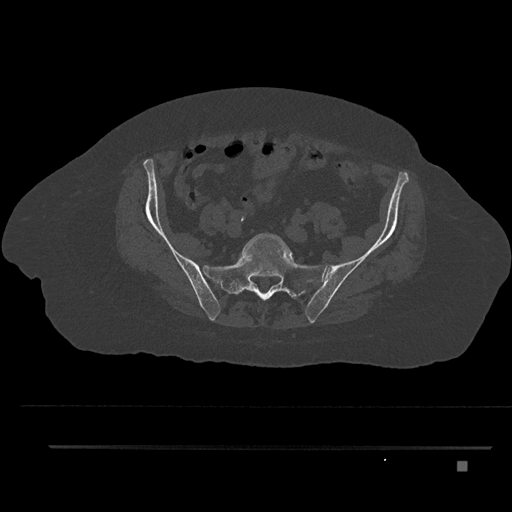
CT including the spine, one axial slice. Slice 8 of 797 in the series (ordered by position). Reconstruction kernel Br40s/3. Bone window (W 1800 / L 400 HU). 512 × 512 image matrix. Female patient, age 76 years. Case-level facts recorded for this patient, not image findings: primary cancer: lung; vertebrae with lytic lesions (as recorded): T11, L3.
Annotated regions visible in this slice (semi-automatically segmented with operator editing):
- L5 vertebra: bounding box [x1, y1, x2, y2] px = [243, 233, 293, 258]